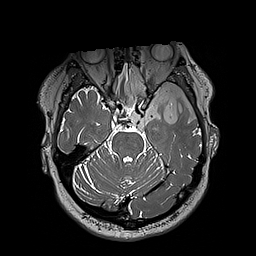
Brain MRI from a brain-tumour surgery series, one axial slice. Position 138 of 192 along the scan axis. 1 mm slice thickness. 256 × 256 image matrix, field of view 250 × 250 mm. Case-level facts recorded for this patient, not image findings: histopathology: Oligodendroglioma; WHO grade: 3; IDH mutation: yes.
Outlined on this slice (expert manual segmentation):
- tumour: bounding box [x1, y1, x2, y2] px = [124, 65, 197, 124]